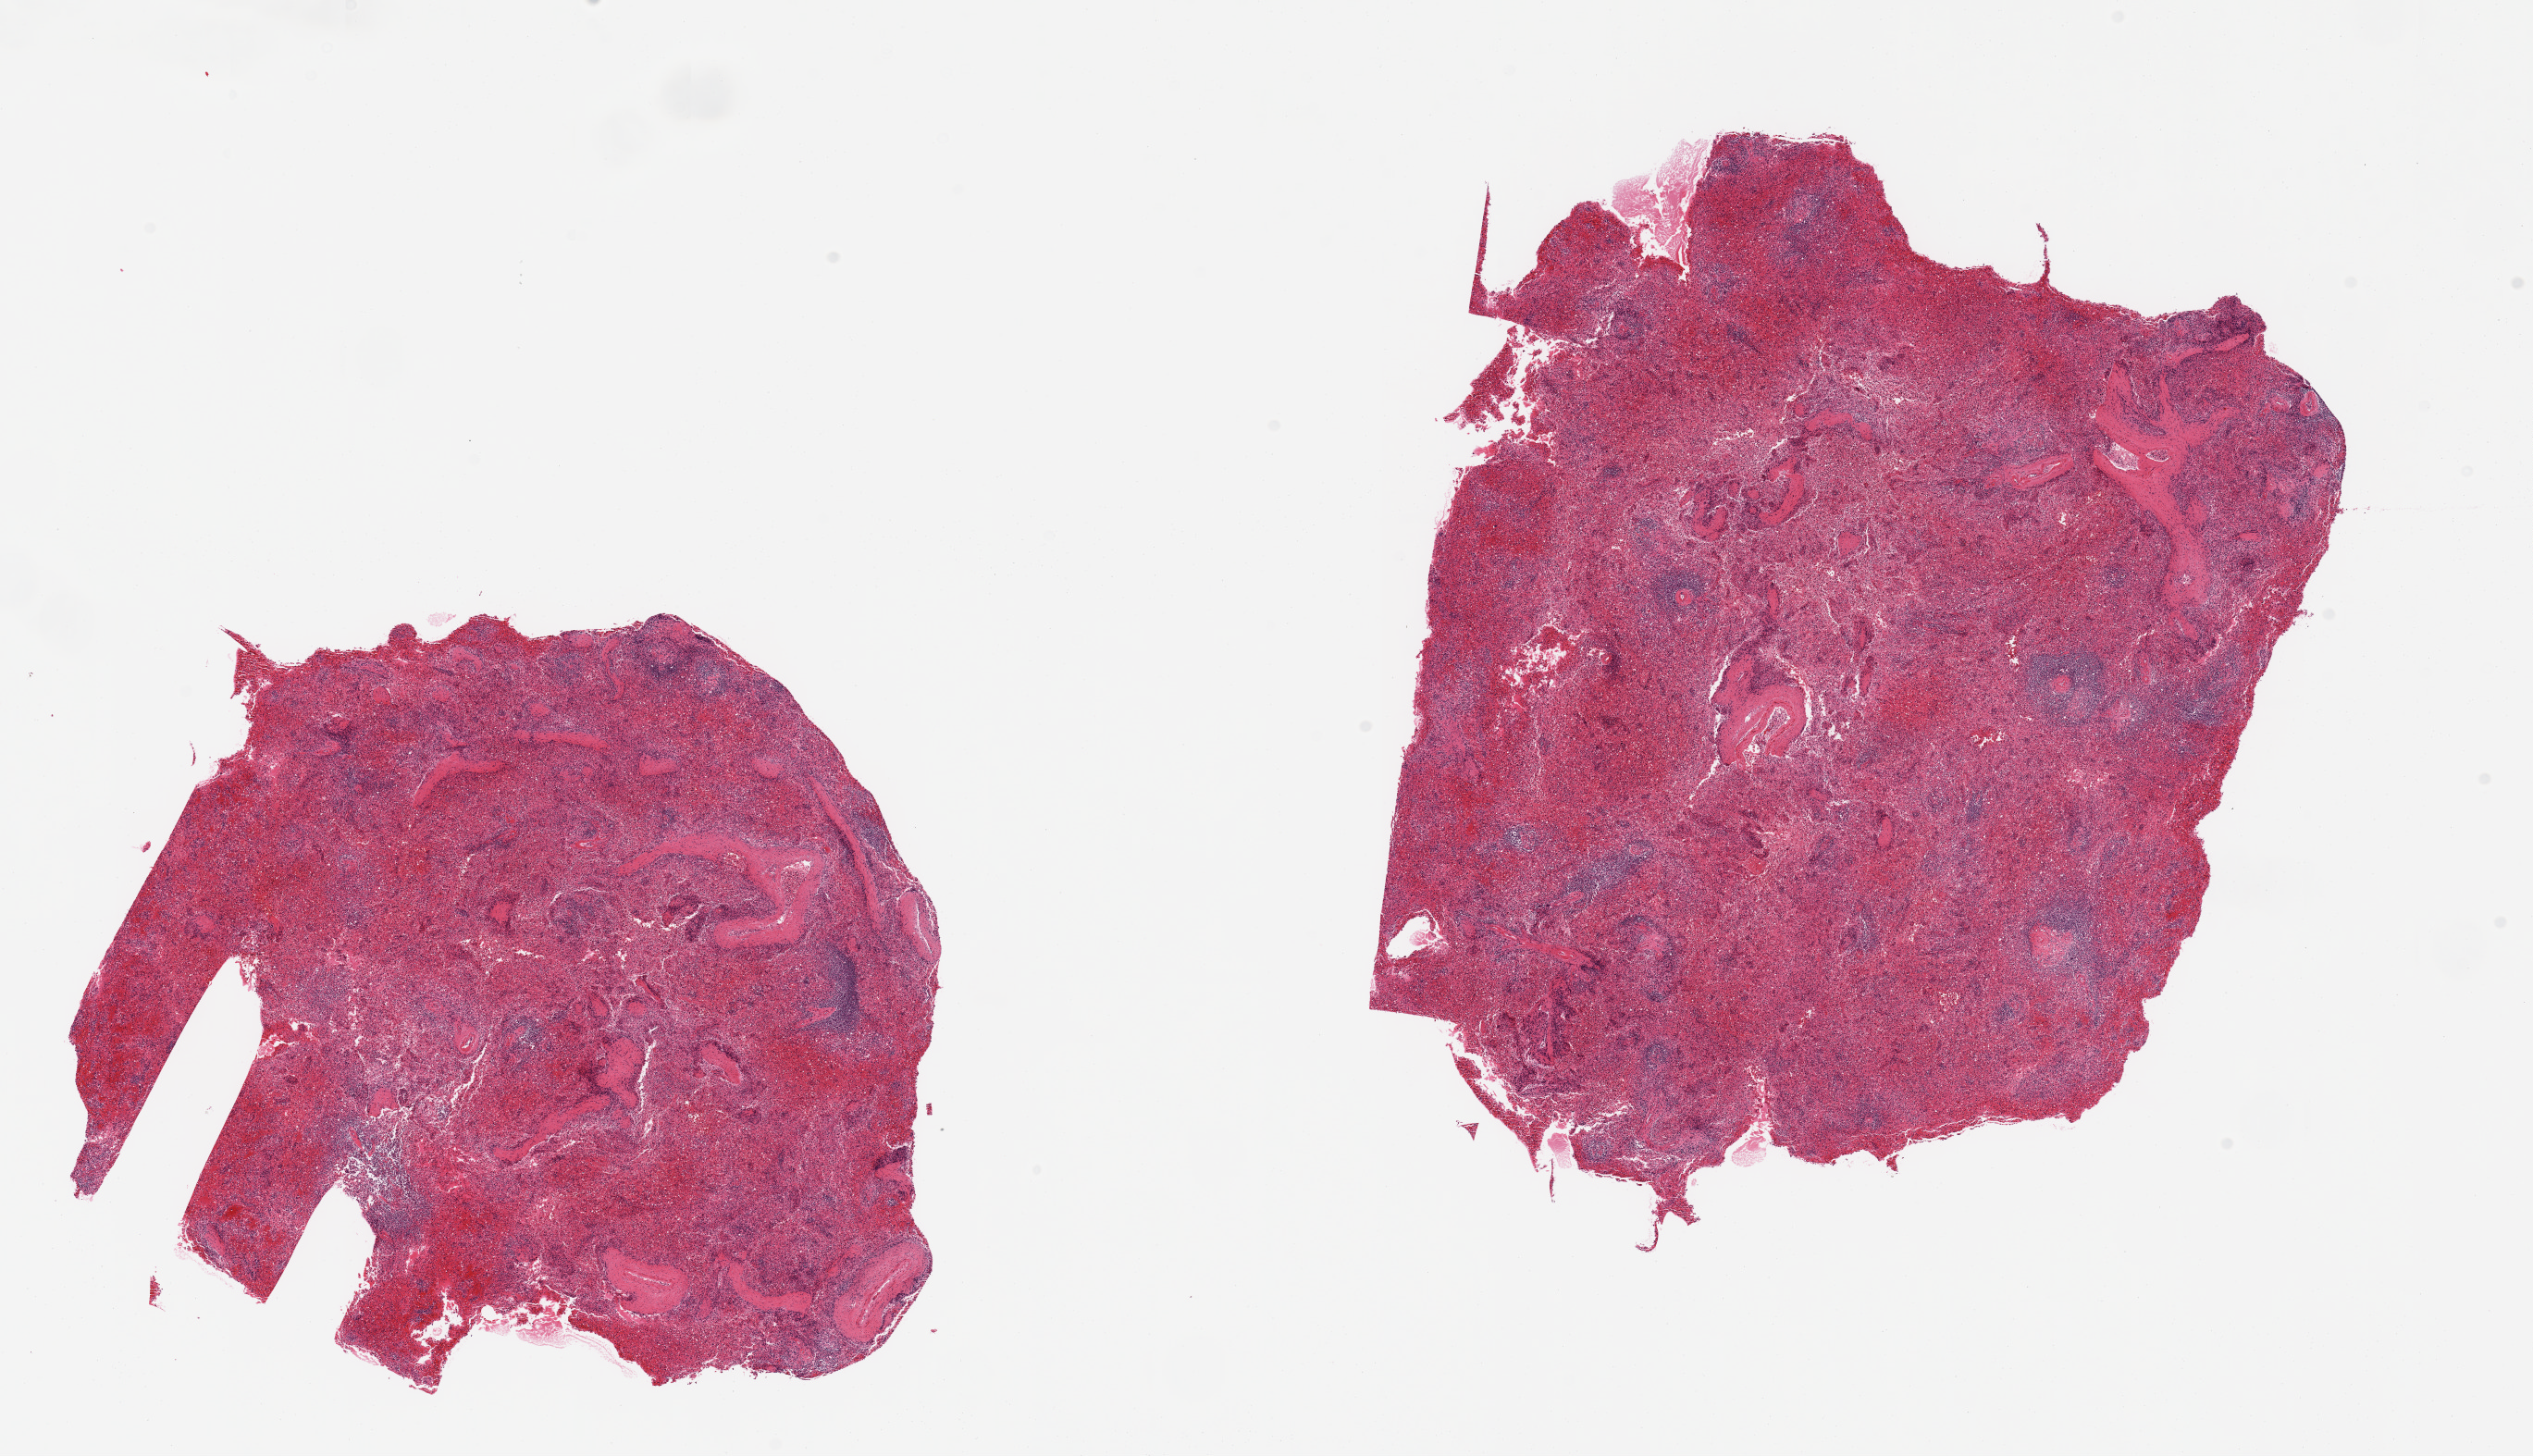
Haematoxylin and eosin whole-slide image, brightfield — whole scanned area (about 21.7 x 12.5 mm, slide scanned at 20x) shown as a low-resolution overview, PAXgene-fixed paraffin-embedded (PFPE) section, target tissue: spleen, donor tissue sample.
Reviewer comment on this tissue sample: 2 pieces; very congested red pulp.